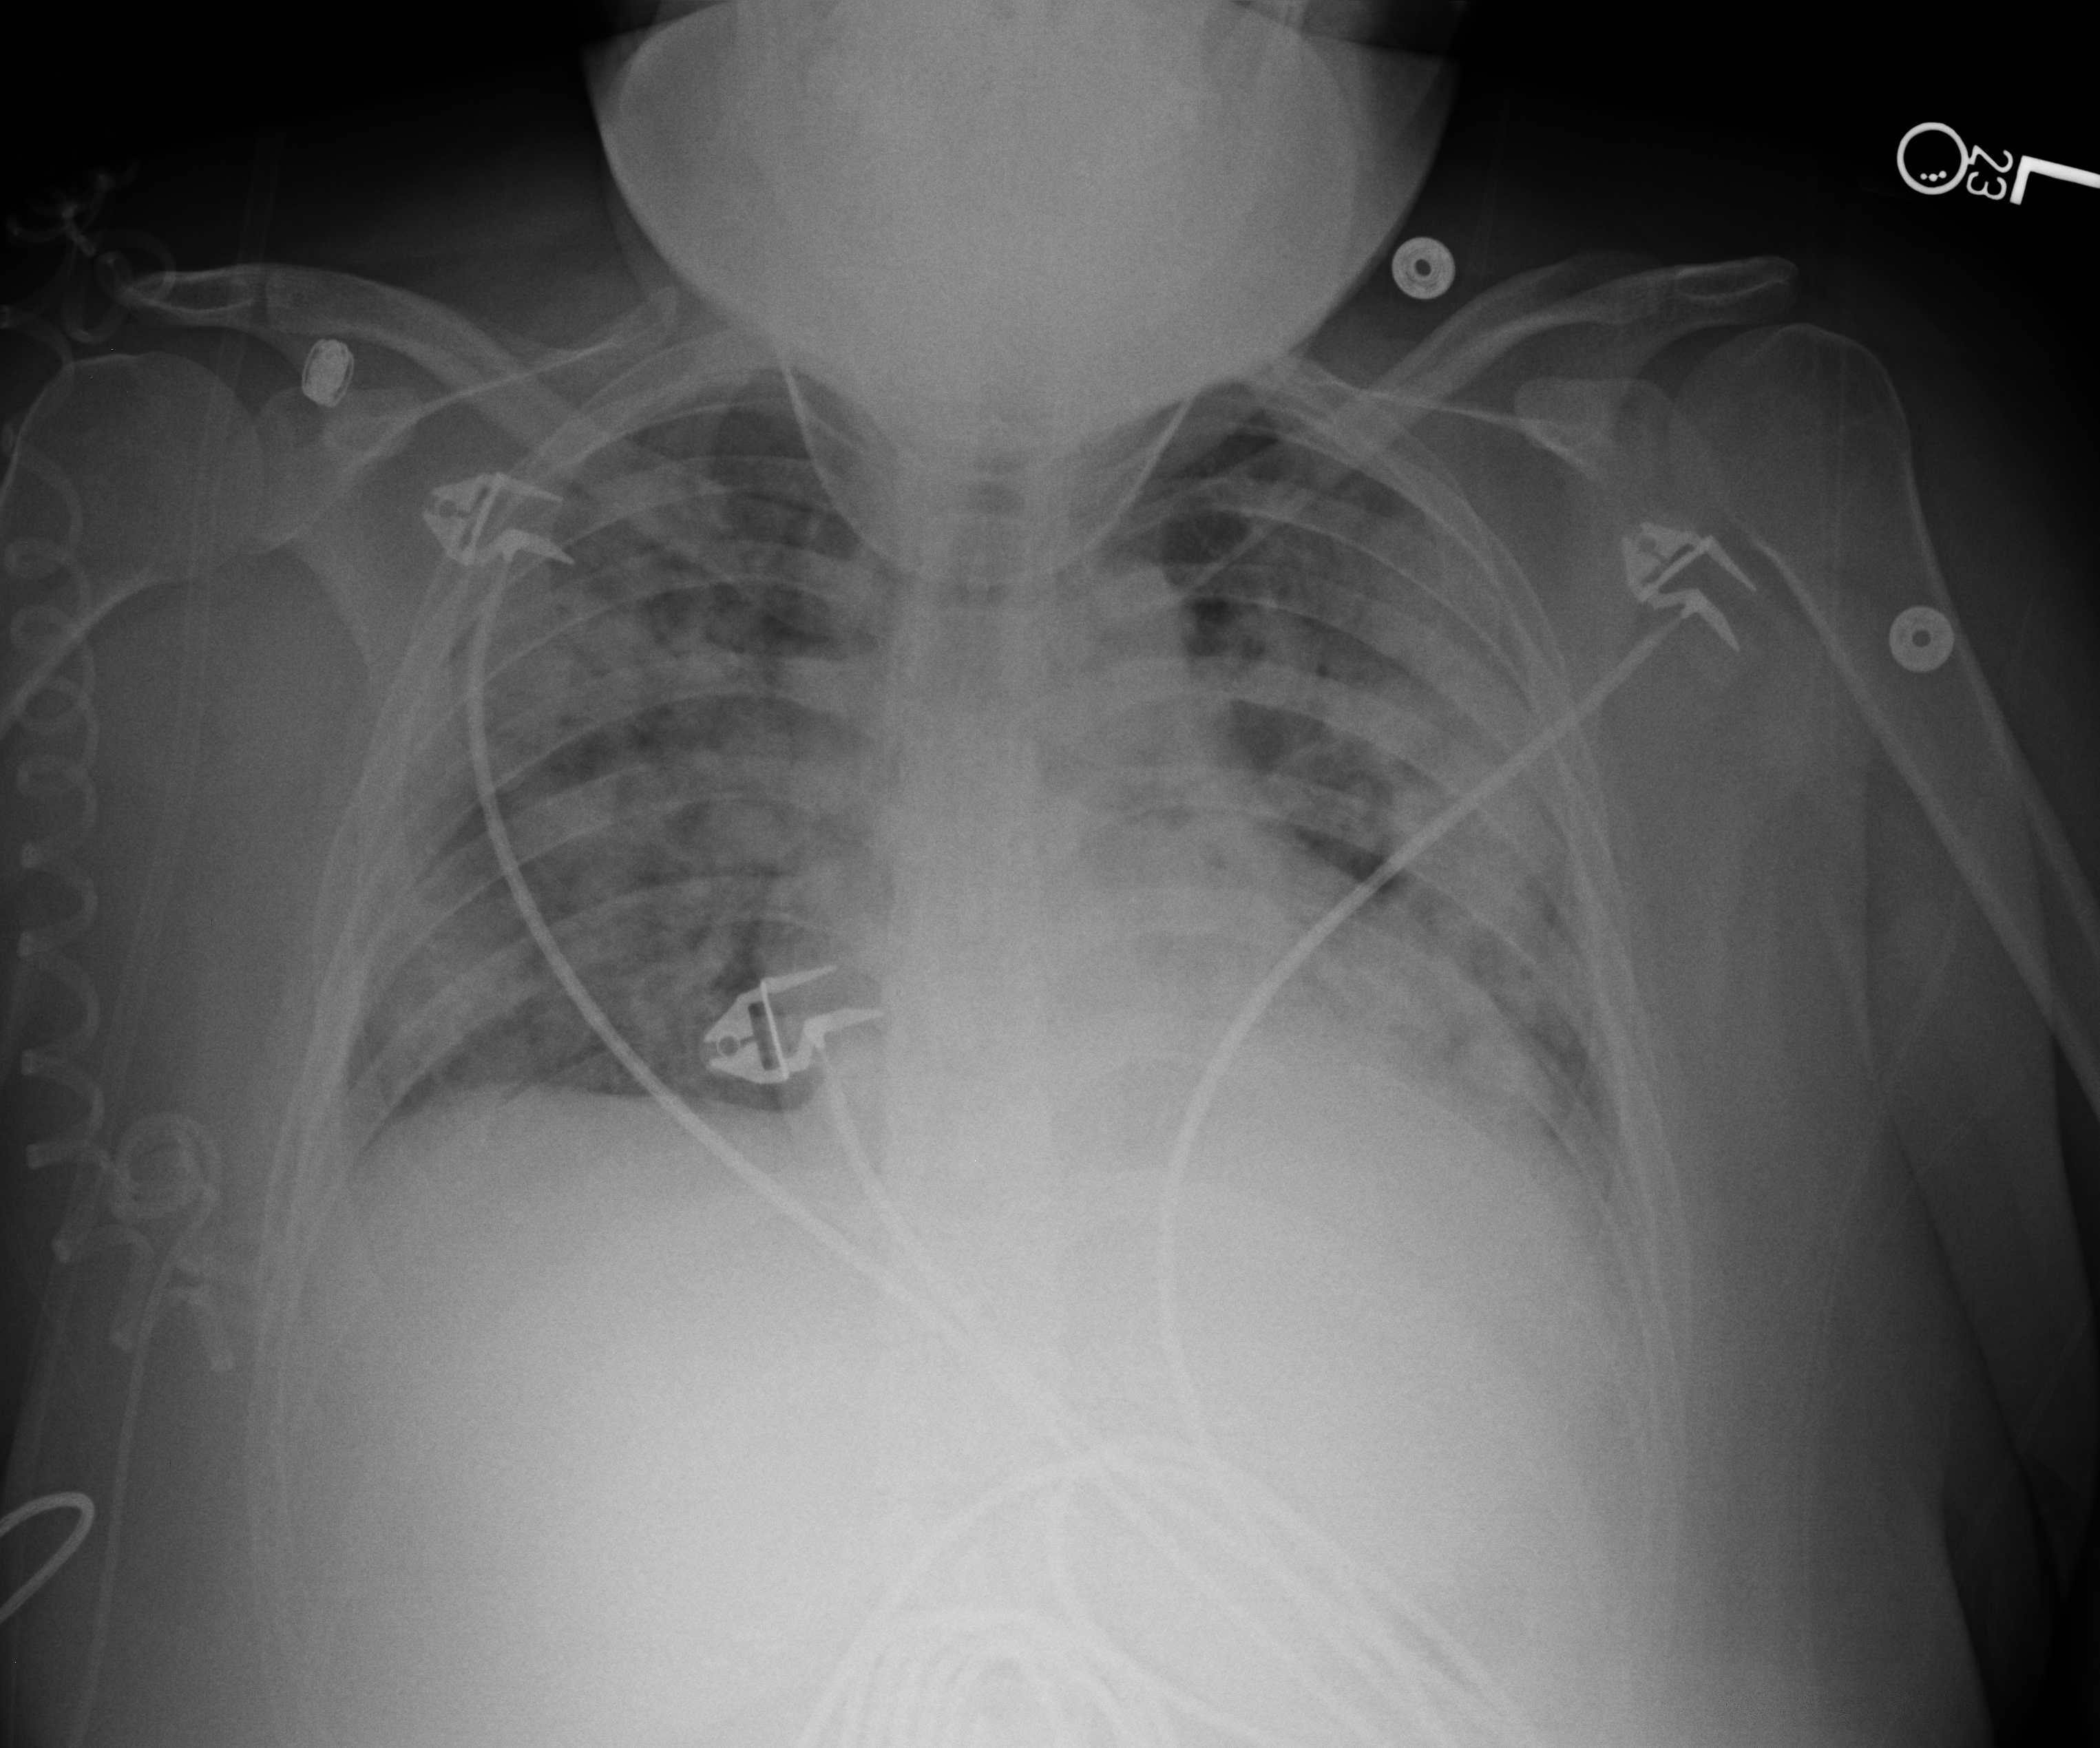
Portable chest radiograph, anteroposterior (AP) projection. Female patient hospitalised with COVID-19, age 18–59 years.
Hospital-stay facts (about this admission, not read from this image; timing relative to this image not recorded): hypertension (admission record): no.